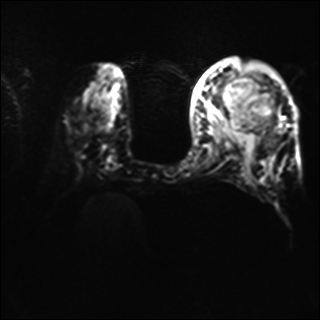
Breast MRI, one axial slice; slice 17 of 40 in the series (ordered by position); diffusion-weighted series; image 2 of 4 stored at this slice position (different b-values; order by instance number); 1.5 T; 320 × 320 image matrix, field of view 320 × 320 mm. Female patient.
Annotated regions visible in this slice (outlined manually by an expert reader):
- tumour on diffusion-weighted imaging: box from (x=218, y=84) to (x=225, y=105) px